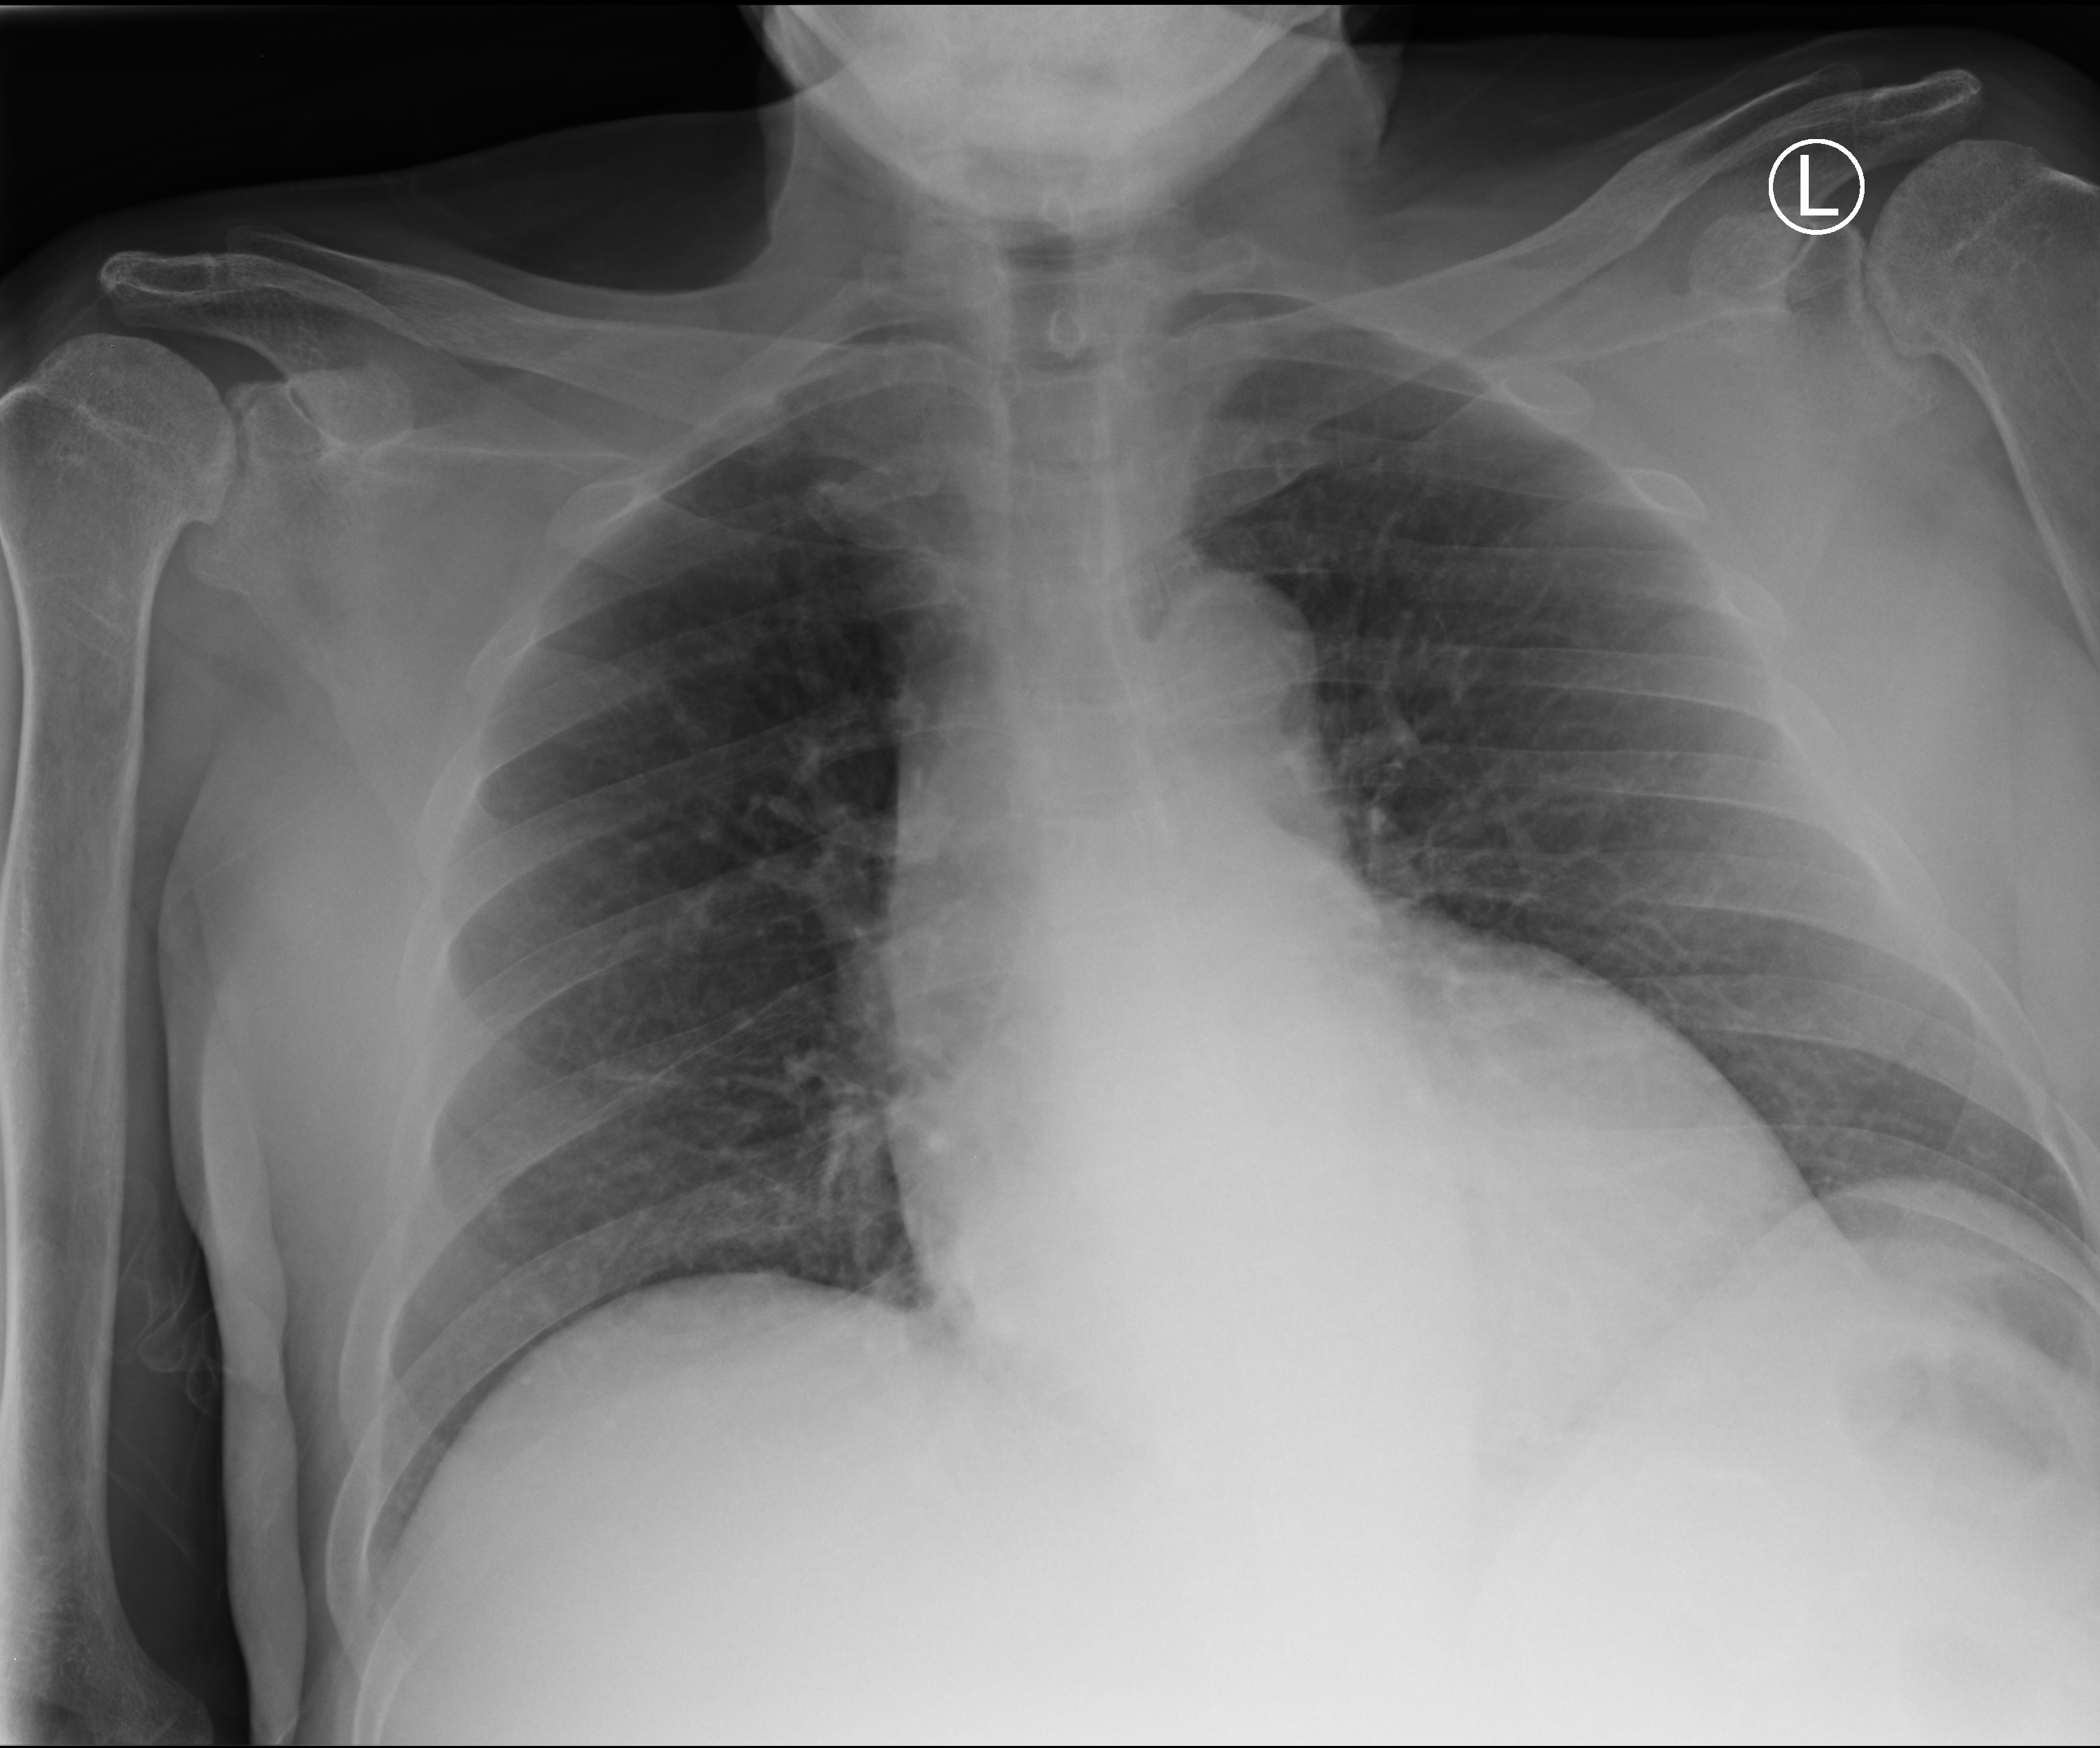
Chest X-ray (portable), anteroposterior (AP) projection. Male patient hospitalised with COVID-19, age 60–74 years.
Hospital-stay facts (about this admission, not read from this image; timing relative to this image not recorded):
- mechanically ventilated during this hospital stay: yes
- admitted to intensive care during this hospital stay: yes